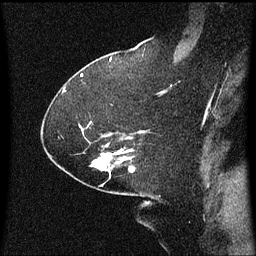
Breast MRI (dynamic contrast-enhanced), one sagittal slice. Slice 38 of 60 in the series (ordered by position). Dynamic contrast-enhanced series, image 2 of 3 at this slice position (ordered by acquisition). 1.5 T. TE 4.2 ms, TR 8 ms. 2.1 mm slice thickness. 256 × 256 image matrix, field of view 200 × 200 mm. Patient: female, 59 years.
Structures marked on this image (semi-automatic segmentation, software-assisted and operator-edited):
- analysis volume of interest (the breast-tissue region the enhancement analysis was run in; not a lesion): box from (x=84, y=140) to (x=135, y=173) px
- tumour enhancement mask (voxels above the 70 % enhancement threshold inside the analysis volume of interest): (x=92, y=150)–(x=133, y=169)